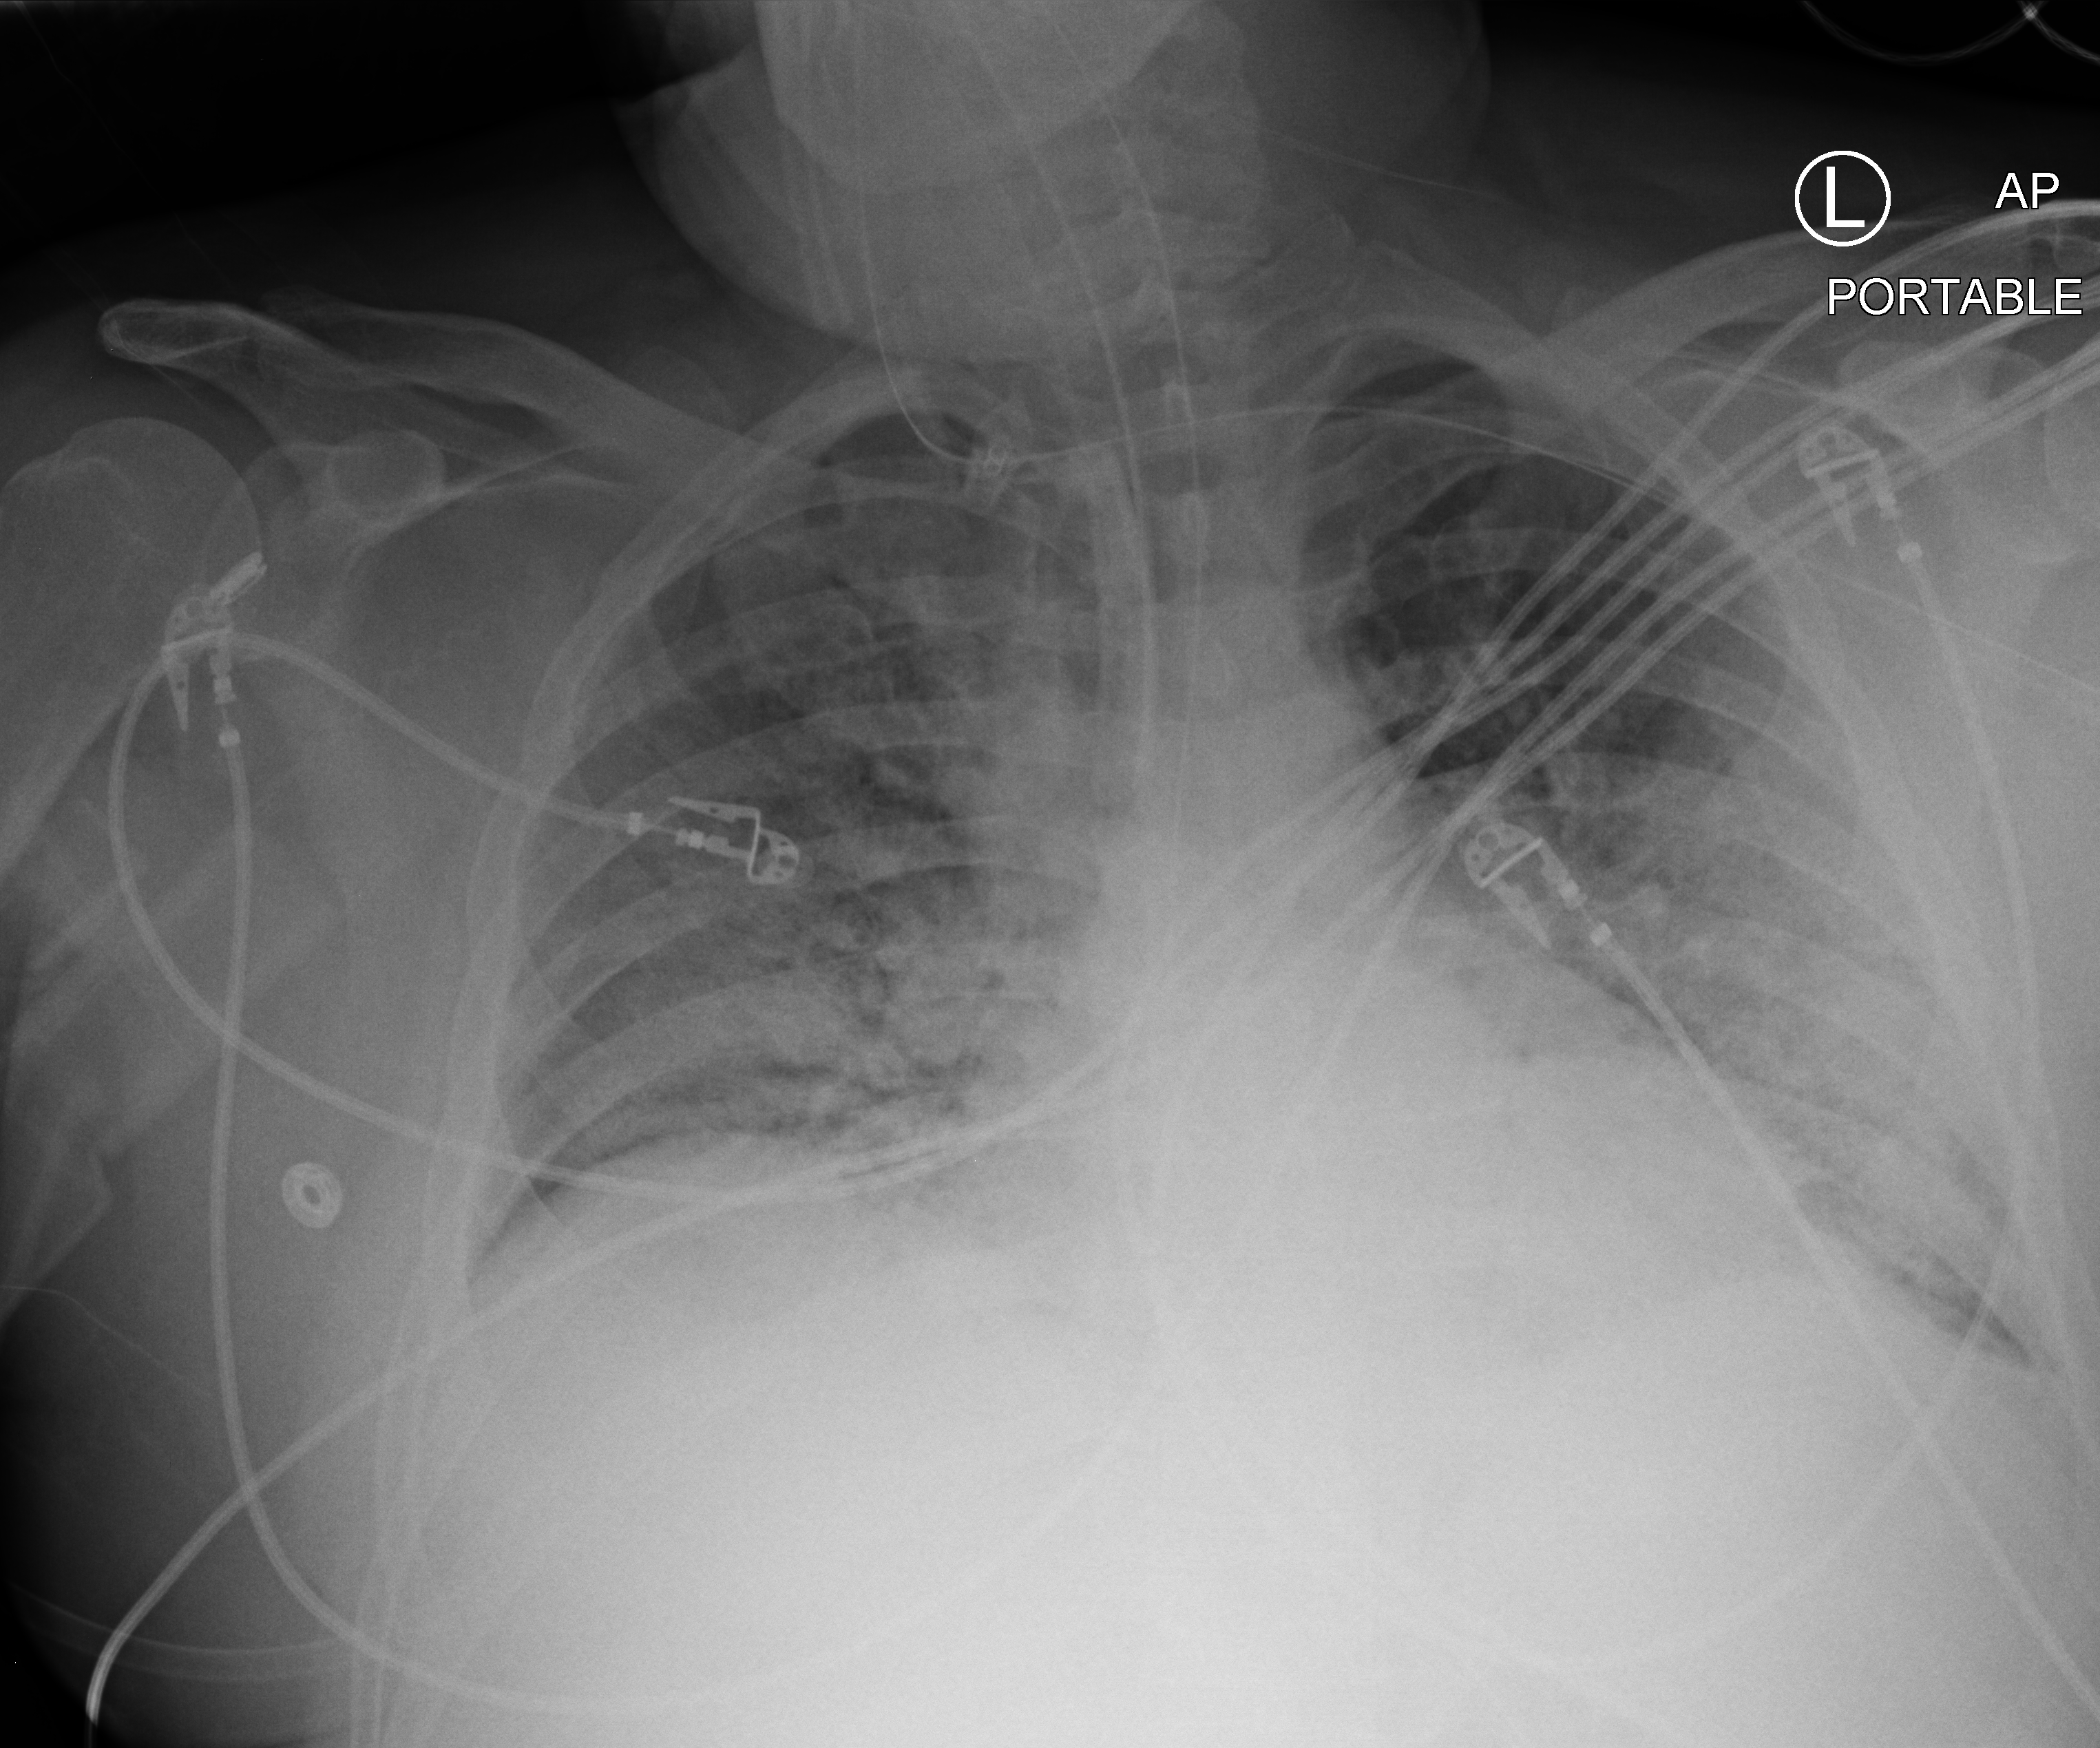
Chest X-ray (portable); anteroposterior (AP) projection. Male patient hospitalised with COVID-19, age 18–59 years.
From the hospital-stay record, not from the radiograph (when in the stay this image was taken is not recorded): COPD (admission record): no.